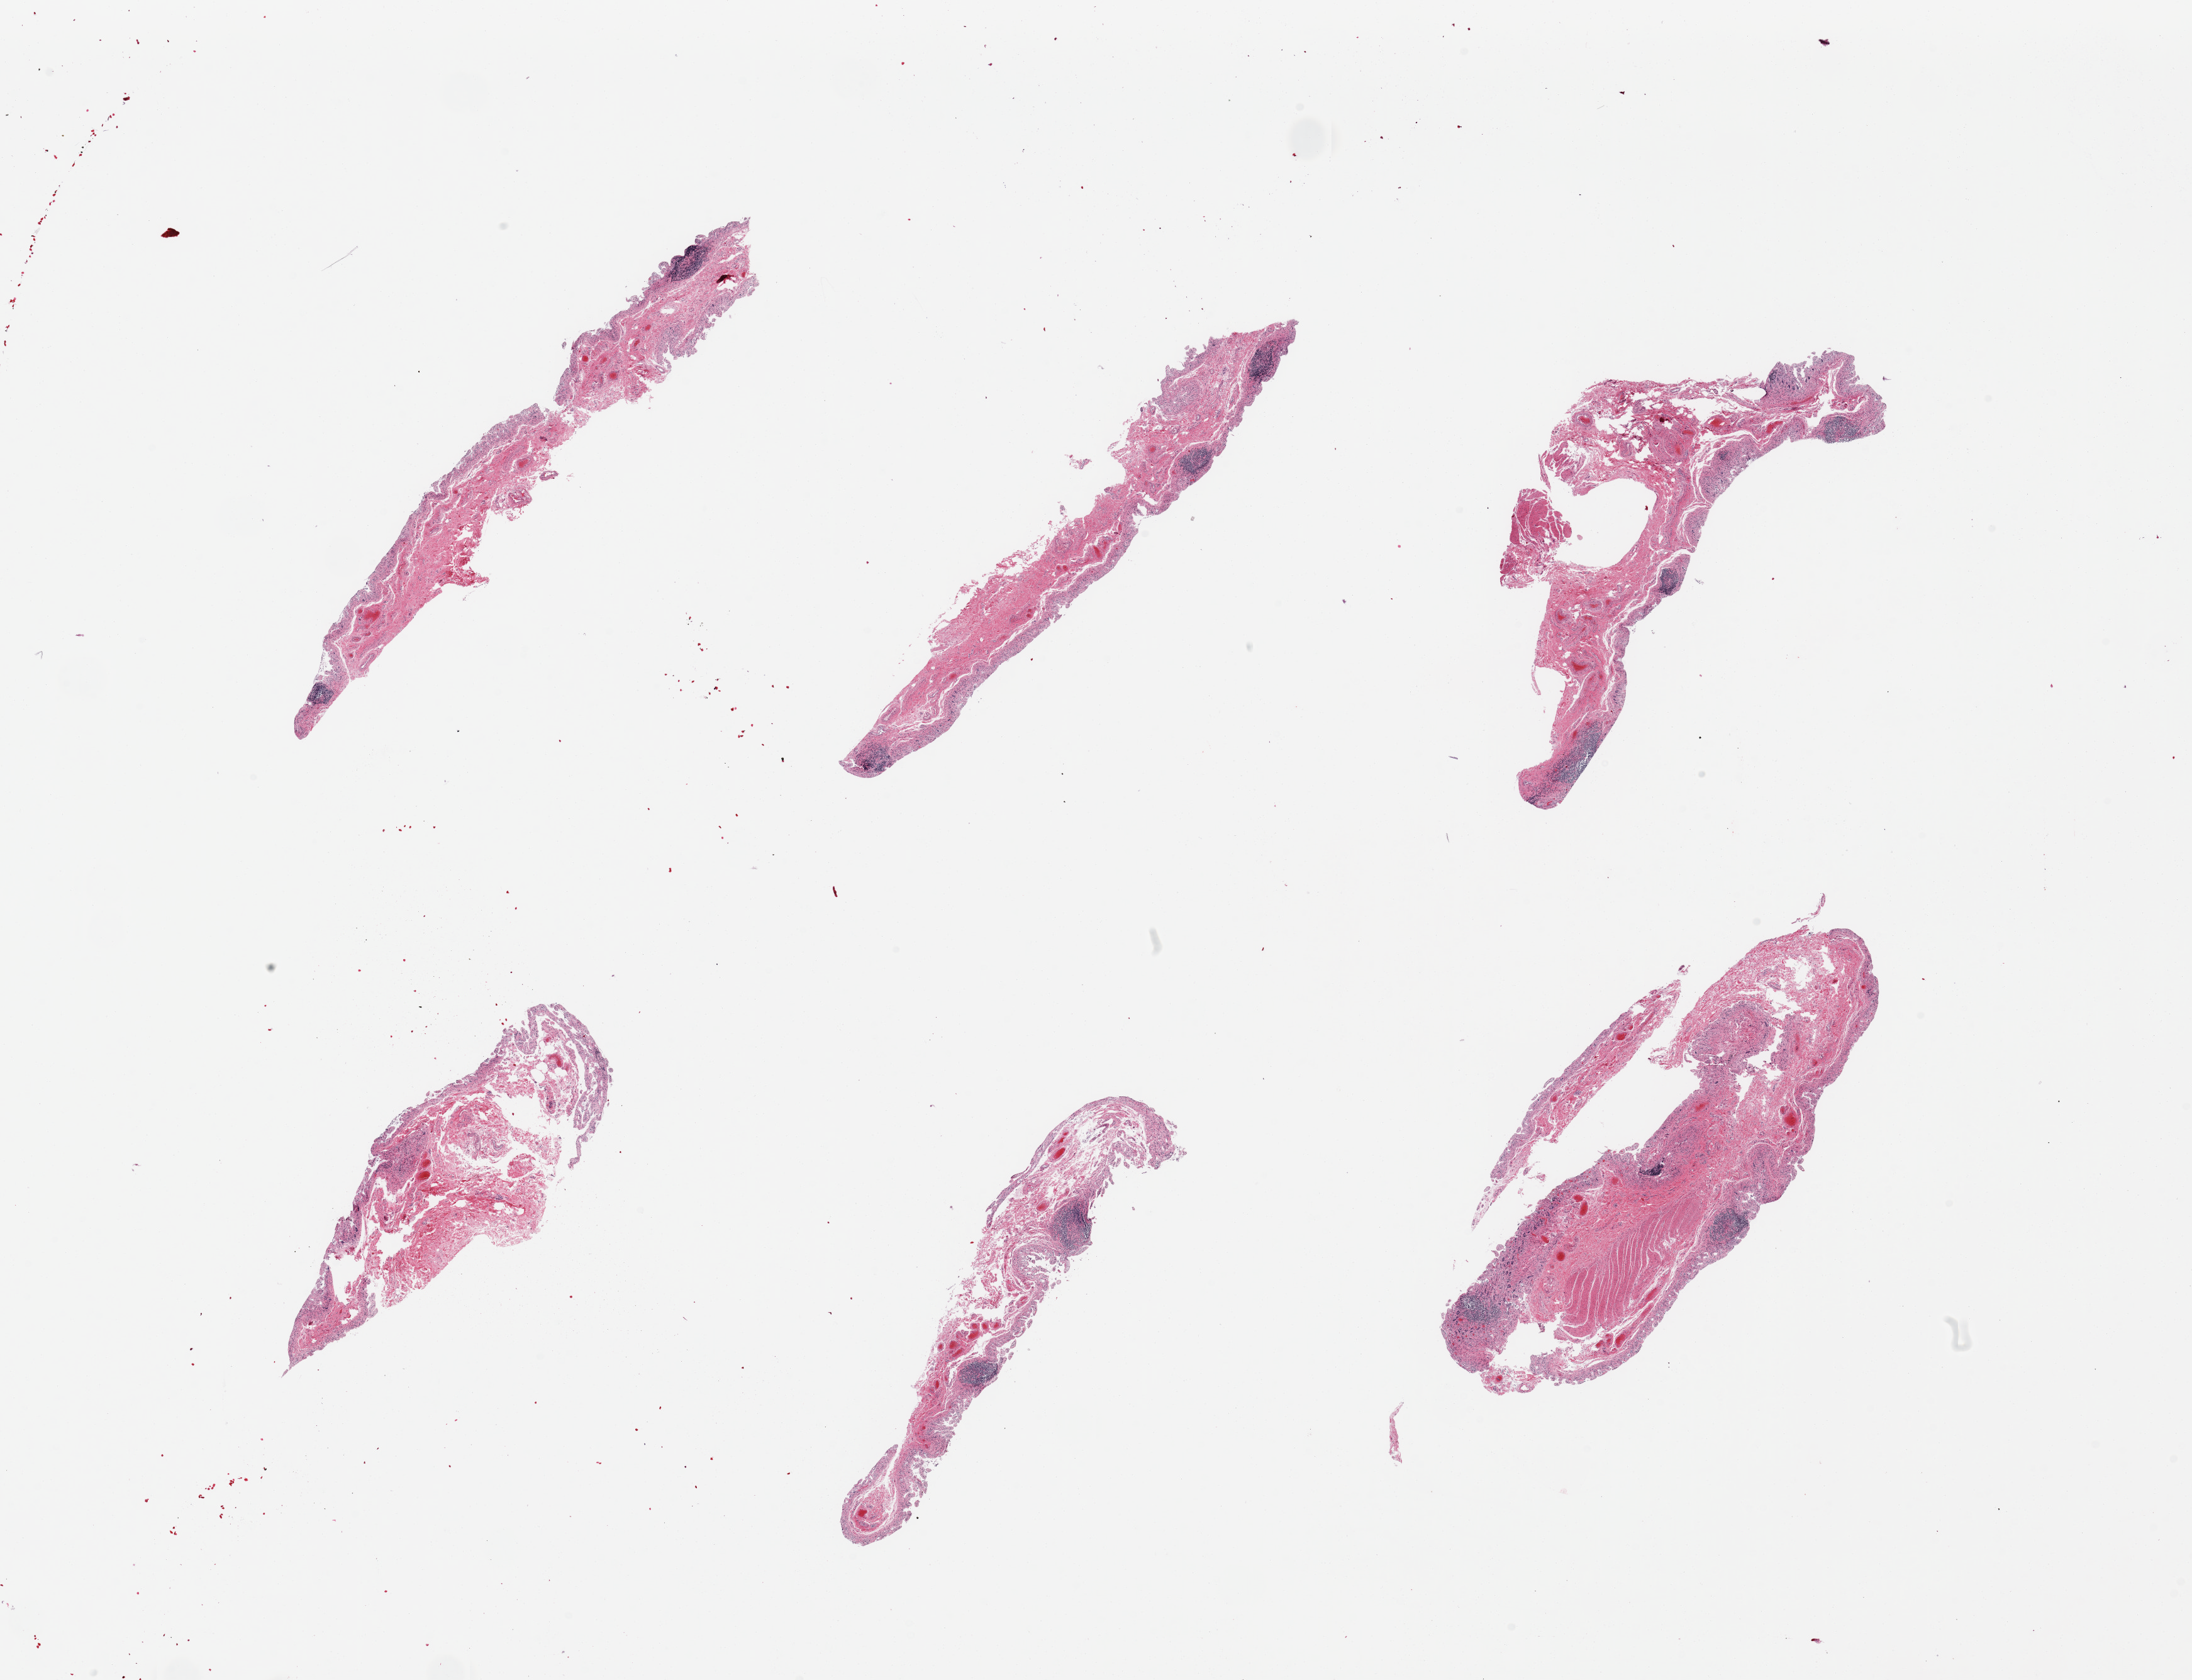
Digitized hematoxylin and eosin (H&E)-stained section, low-resolution overview of the scanned area, about 27.6 x 21.1 mm (from a 20x scan). Donor: male.
Specimen: PAXgene-fixed paraffin-embedded (PFPE) section; target tissue: ileum; donor tissue sample.